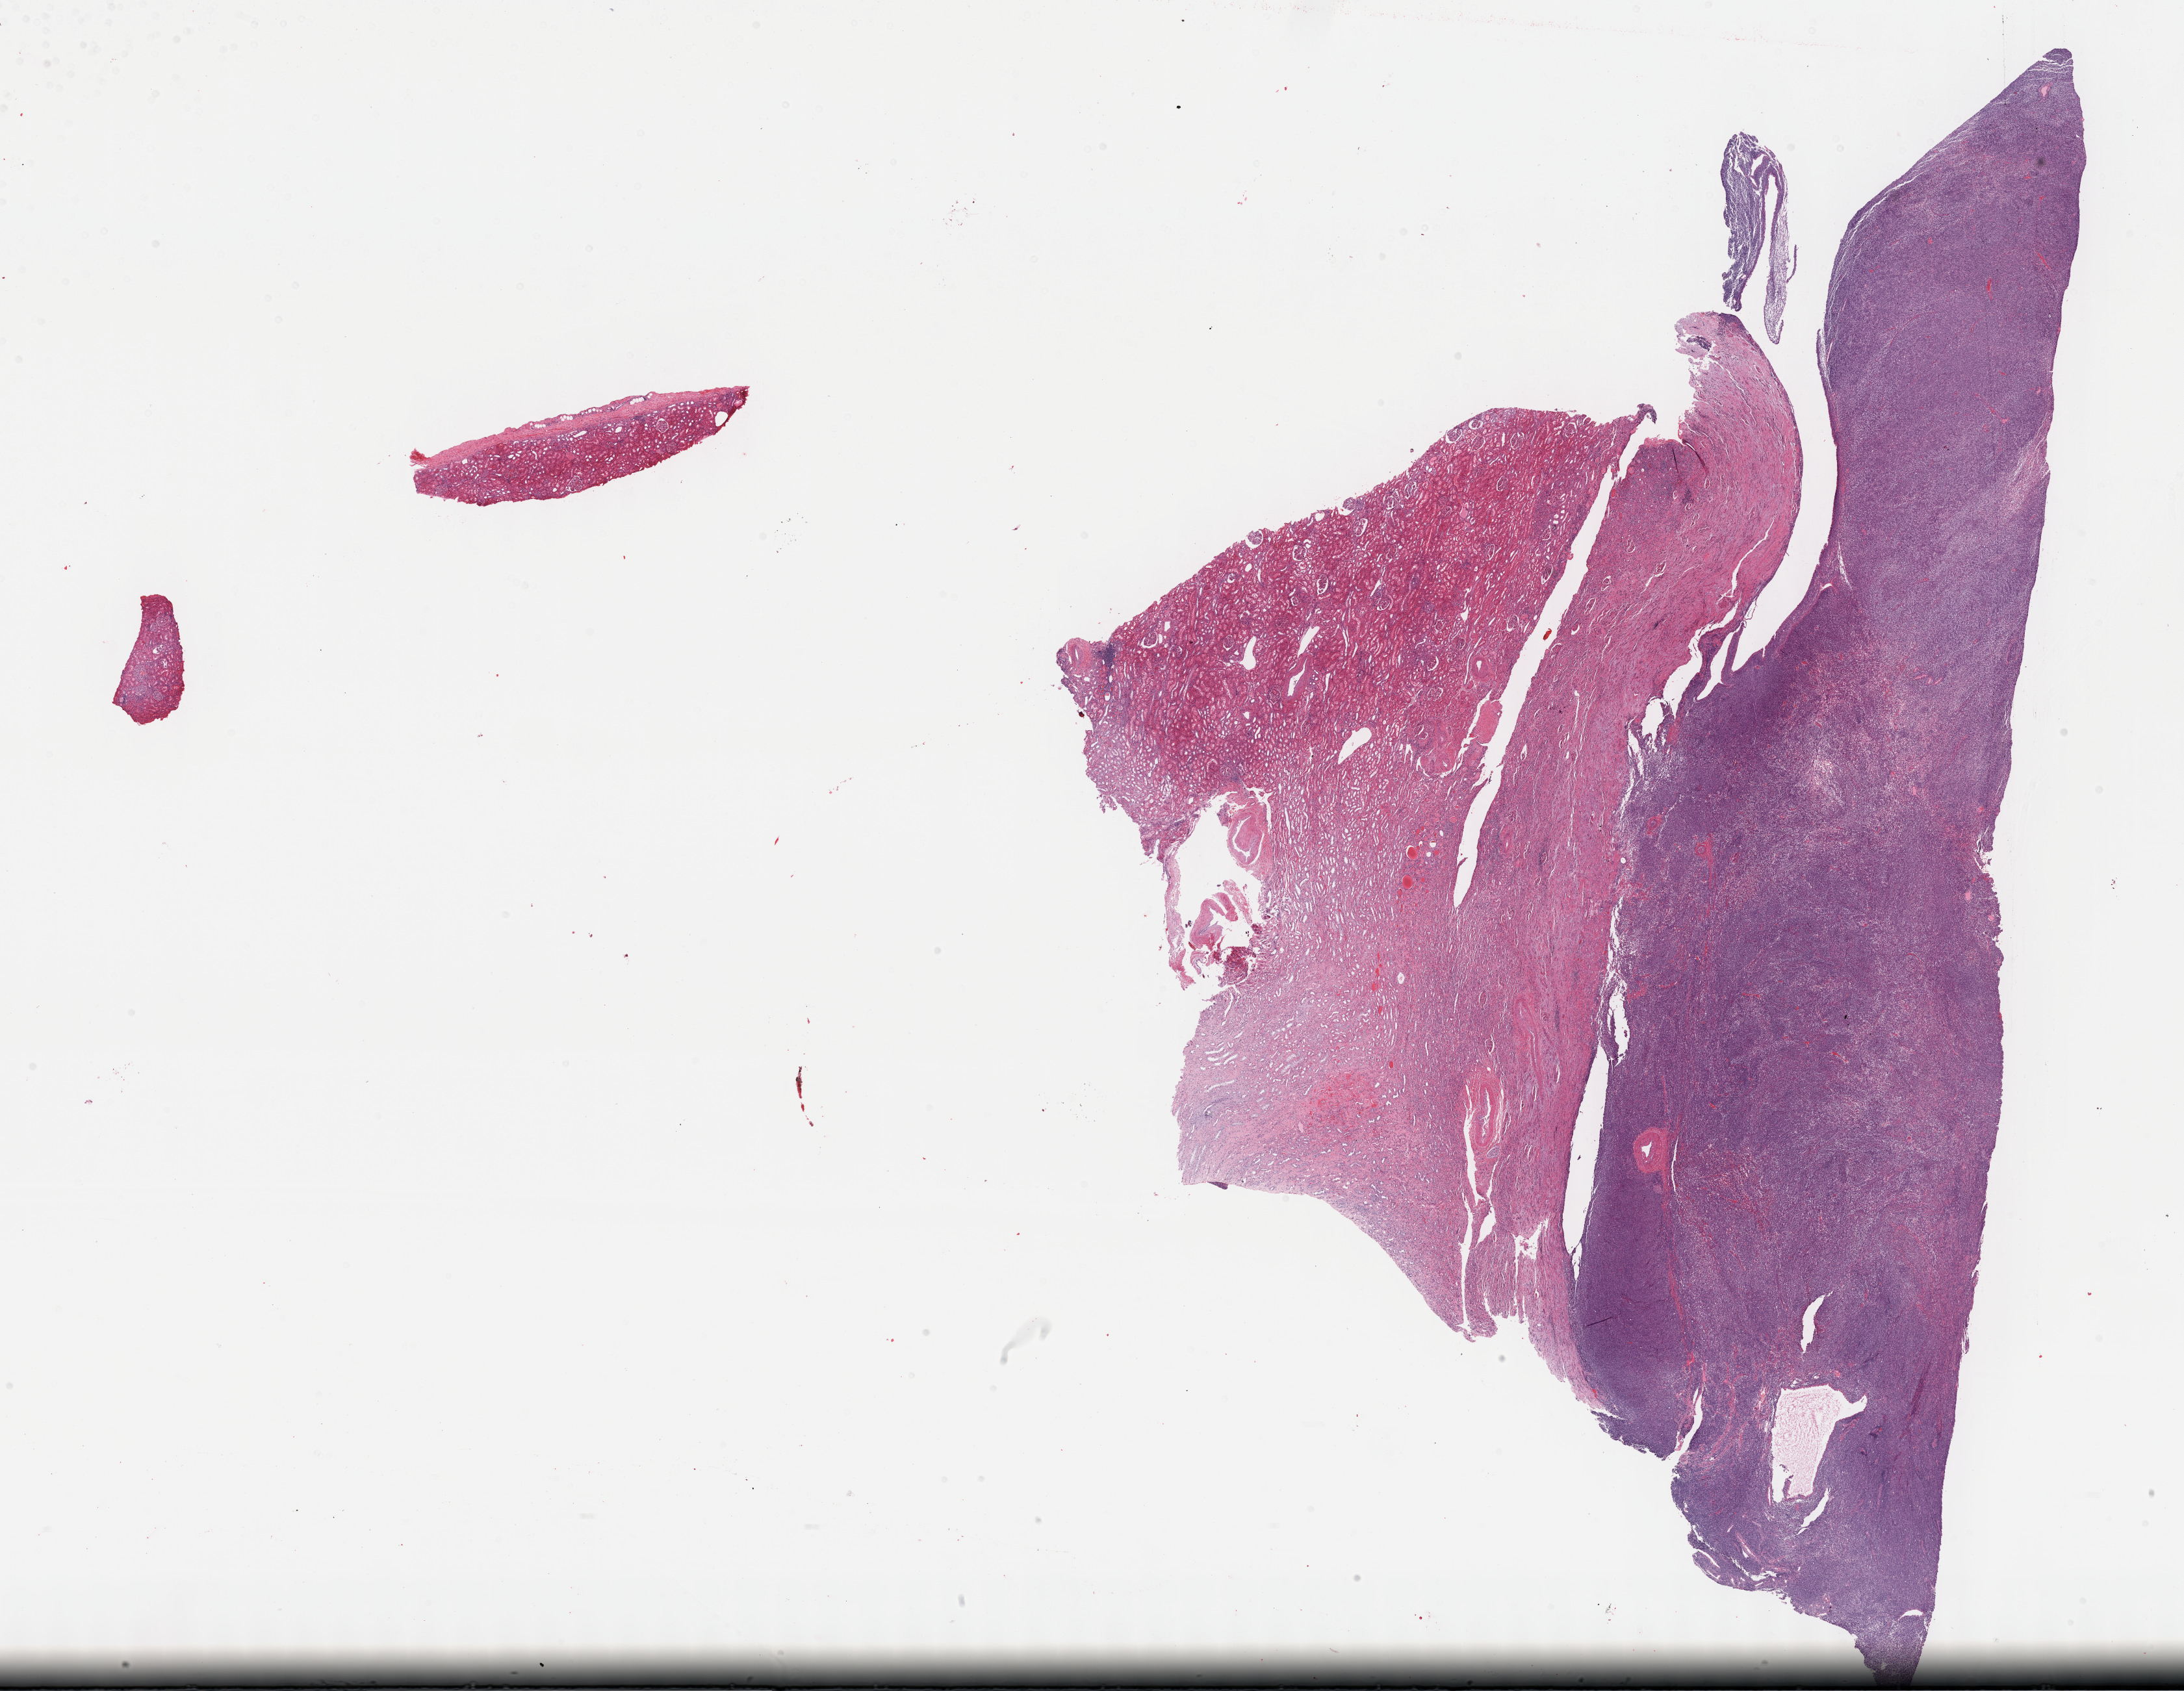
Hematoxylin and eosin (H&E) stained whole-slide image, a low-resolution overview of the entire scanned area, about 27.2 x 21.1 mm (from a 40x scan); formalin-fixed paraffin-embedded (FFPE) diagnostic section; kidney, primary tumour sample. Patient: female, age at initial diagnosis 40 years.
- pathologic diagnosis: Synovial sarcoma, spindle cell